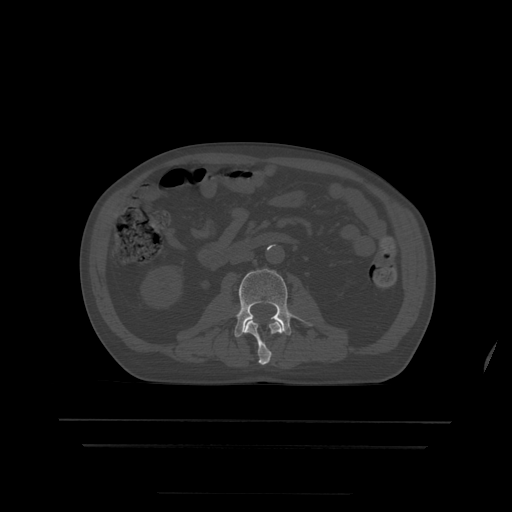
CT including the spine, one axial slice; position 128 of 522 along the scan axis; bone window (W 1800 / L 400 HU); 1.25 mm slice thickness; 512 × 512 image matrix, field of view 436 × 436 mm. Patient age 68 years. Case-level facts recorded for this patient, not image findings: primary cancer: urothelial.
Annotated regions visible in this slice (semi-automatically segmented with operator editing):
- L2 vertebra: bounding box <245,321,282,365> (left, top, right, bottom; pixels)
- L3 vertebra: <221,269,310,338>